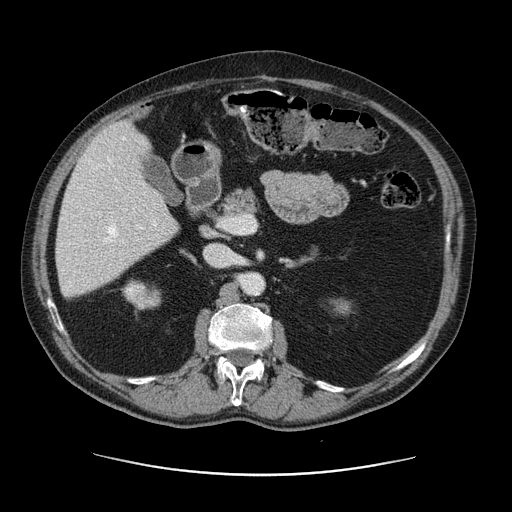
Contrast-enhanced abdominal CT, one axial slice; slice 63 of 141 in the series (ordered by position); soft-tissue window (W 400 / L 40 HU); 2.5 mm slice thickness; 512 × 512 image matrix, field of view 395 × 395 mm. Male patient, age 72 years. Case-level facts recorded for this patient, not image findings: diagnosis: colorectal cancer liver metastases, imaged before liver resection; multiple liver metastases: yes; largest metastasis: 5.4 cm; disease in both lobes: yes.
Annotated regions visible in this slice (manually delineated by an expert):
- hepatic veins: bounding box (x1, y1, x2, y2) in pixels: (95, 137, 144, 242)
- liver: (57, 123, 178, 298)
- planned liver remnant (the part of the liver to remain after resection): (57, 185, 178, 298)
- portal vein (with intrahepatic branches): (136, 224, 145, 239)